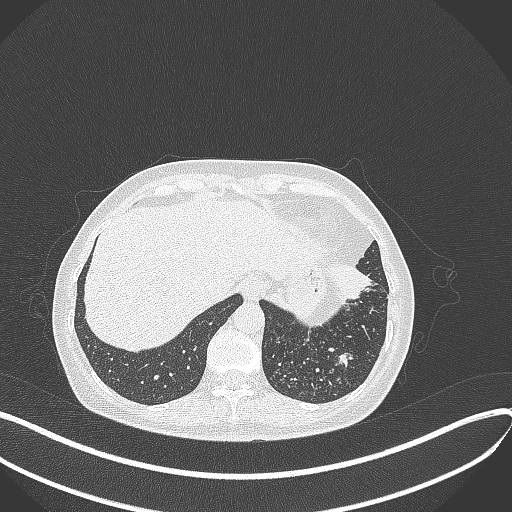
Chest CT, one axial slice; lung window (W 1500 / L -600 HU); 1 mm slice thickness; 512 × 512 image matrix. Patient: female, 63 years. Case-level facts recorded for this patient, not image findings: clinical TNM (as recorded): T1b N0 M0; histopathological grade: G2-3.
Outlined on this slice (rectangle marked by the reading radiologist):
- lung tumour (recorded histology: adenocarcinoma): bounding box (x1, y1, x2, y2) in pixels: (324, 261, 374, 308)